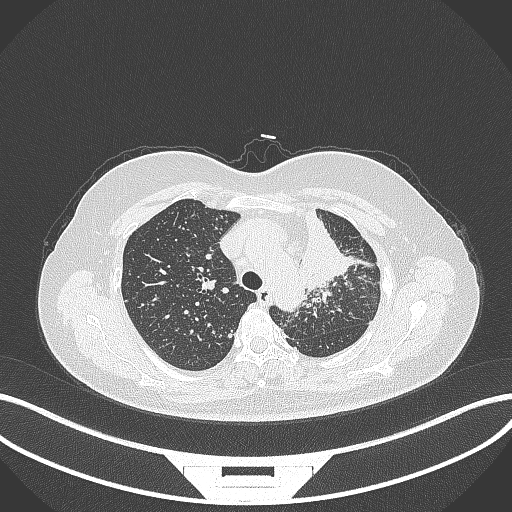
Chest CT, one axial slice; slice 251 of 348 in the series (ordered by position); 120 kVp; lung window (W 1500 / L -600 HU); 1 mm slice thickness; 512 × 512 image matrix. Patient: female, 49 years. From the clinical record (not read from this slice): clinical TNM (as recorded): T1c N0 M1.
Structures marked on this image (rectangle marked by the reading radiologist):
- lung tumour (recorded histology: adenocarcinoma): box from (x=298, y=205) to (x=357, y=294) px